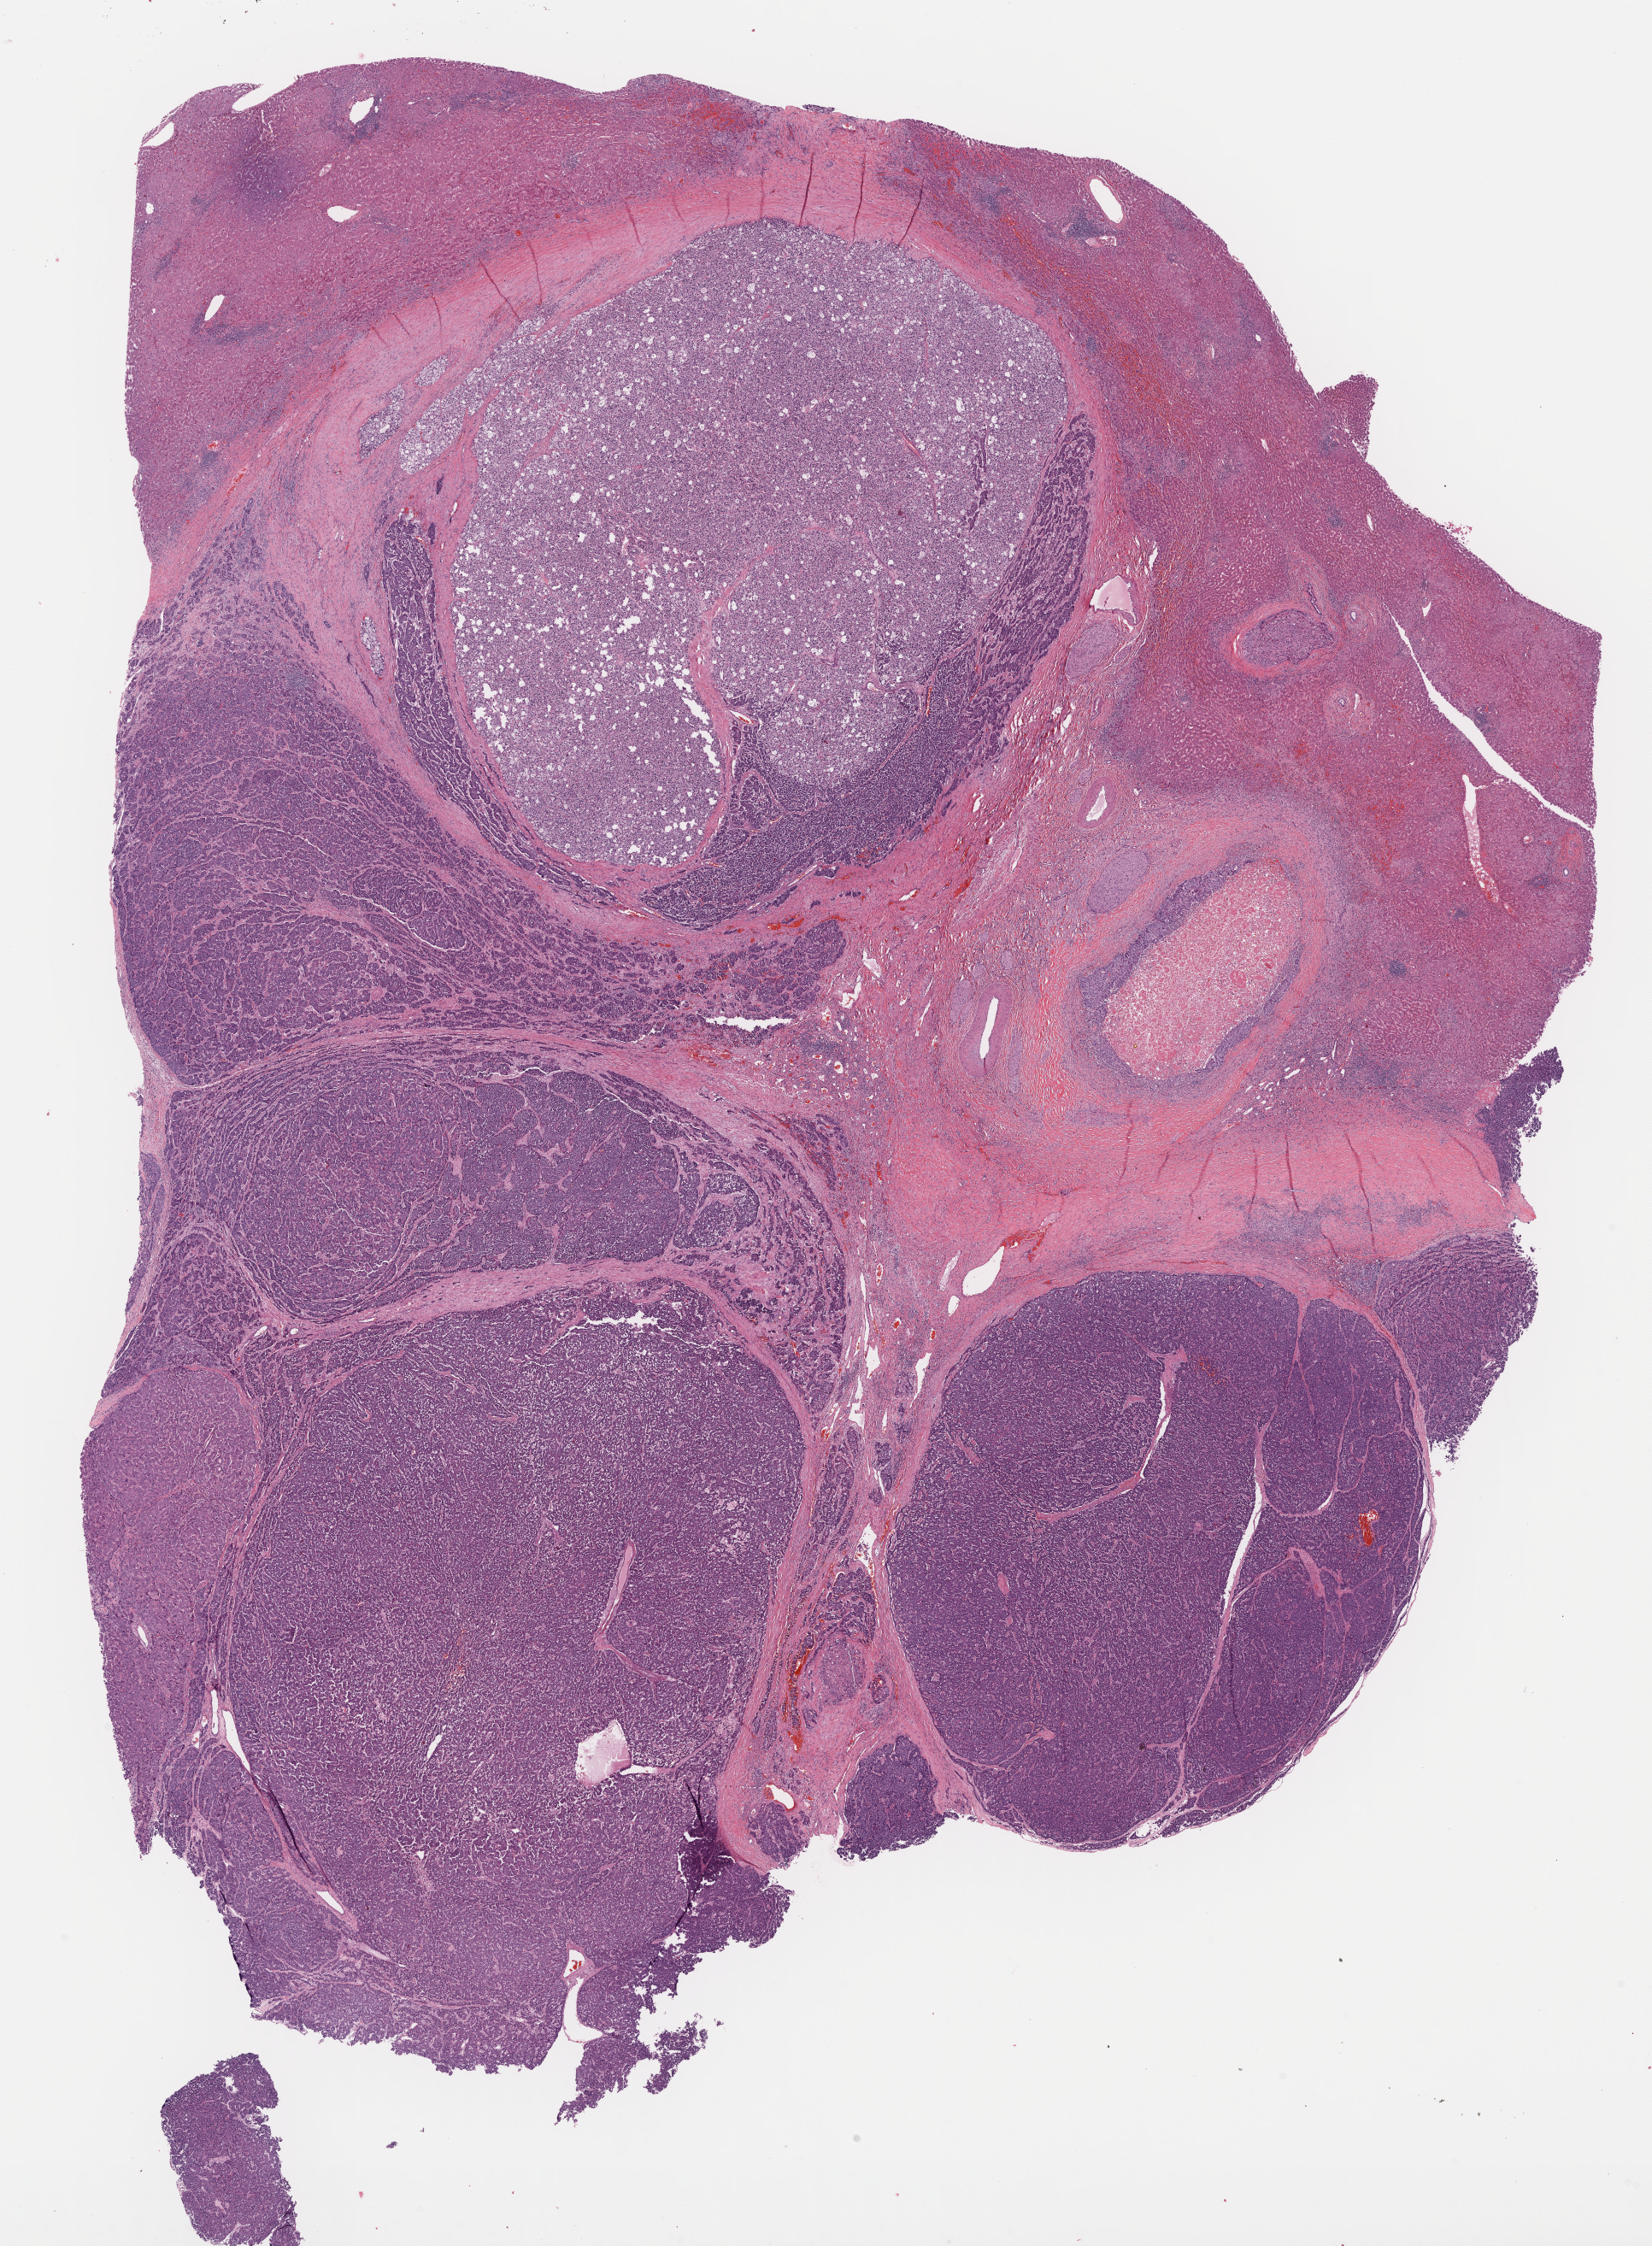
H&E-stained whole-slide image — low-resolution overview of the scanned area, about 15.6 x 21.3 mm (slide scanned at 40x), FFPE section, liver, primary tumour sample. Female patient; age at initial diagnosis 55 years. Histologic grade: G3 (poorly differentiated).
- TNM: T2 N0 M0
- diagnosis: Hepatocellular carcinoma, NOS
- AJCC pathologic stage: II